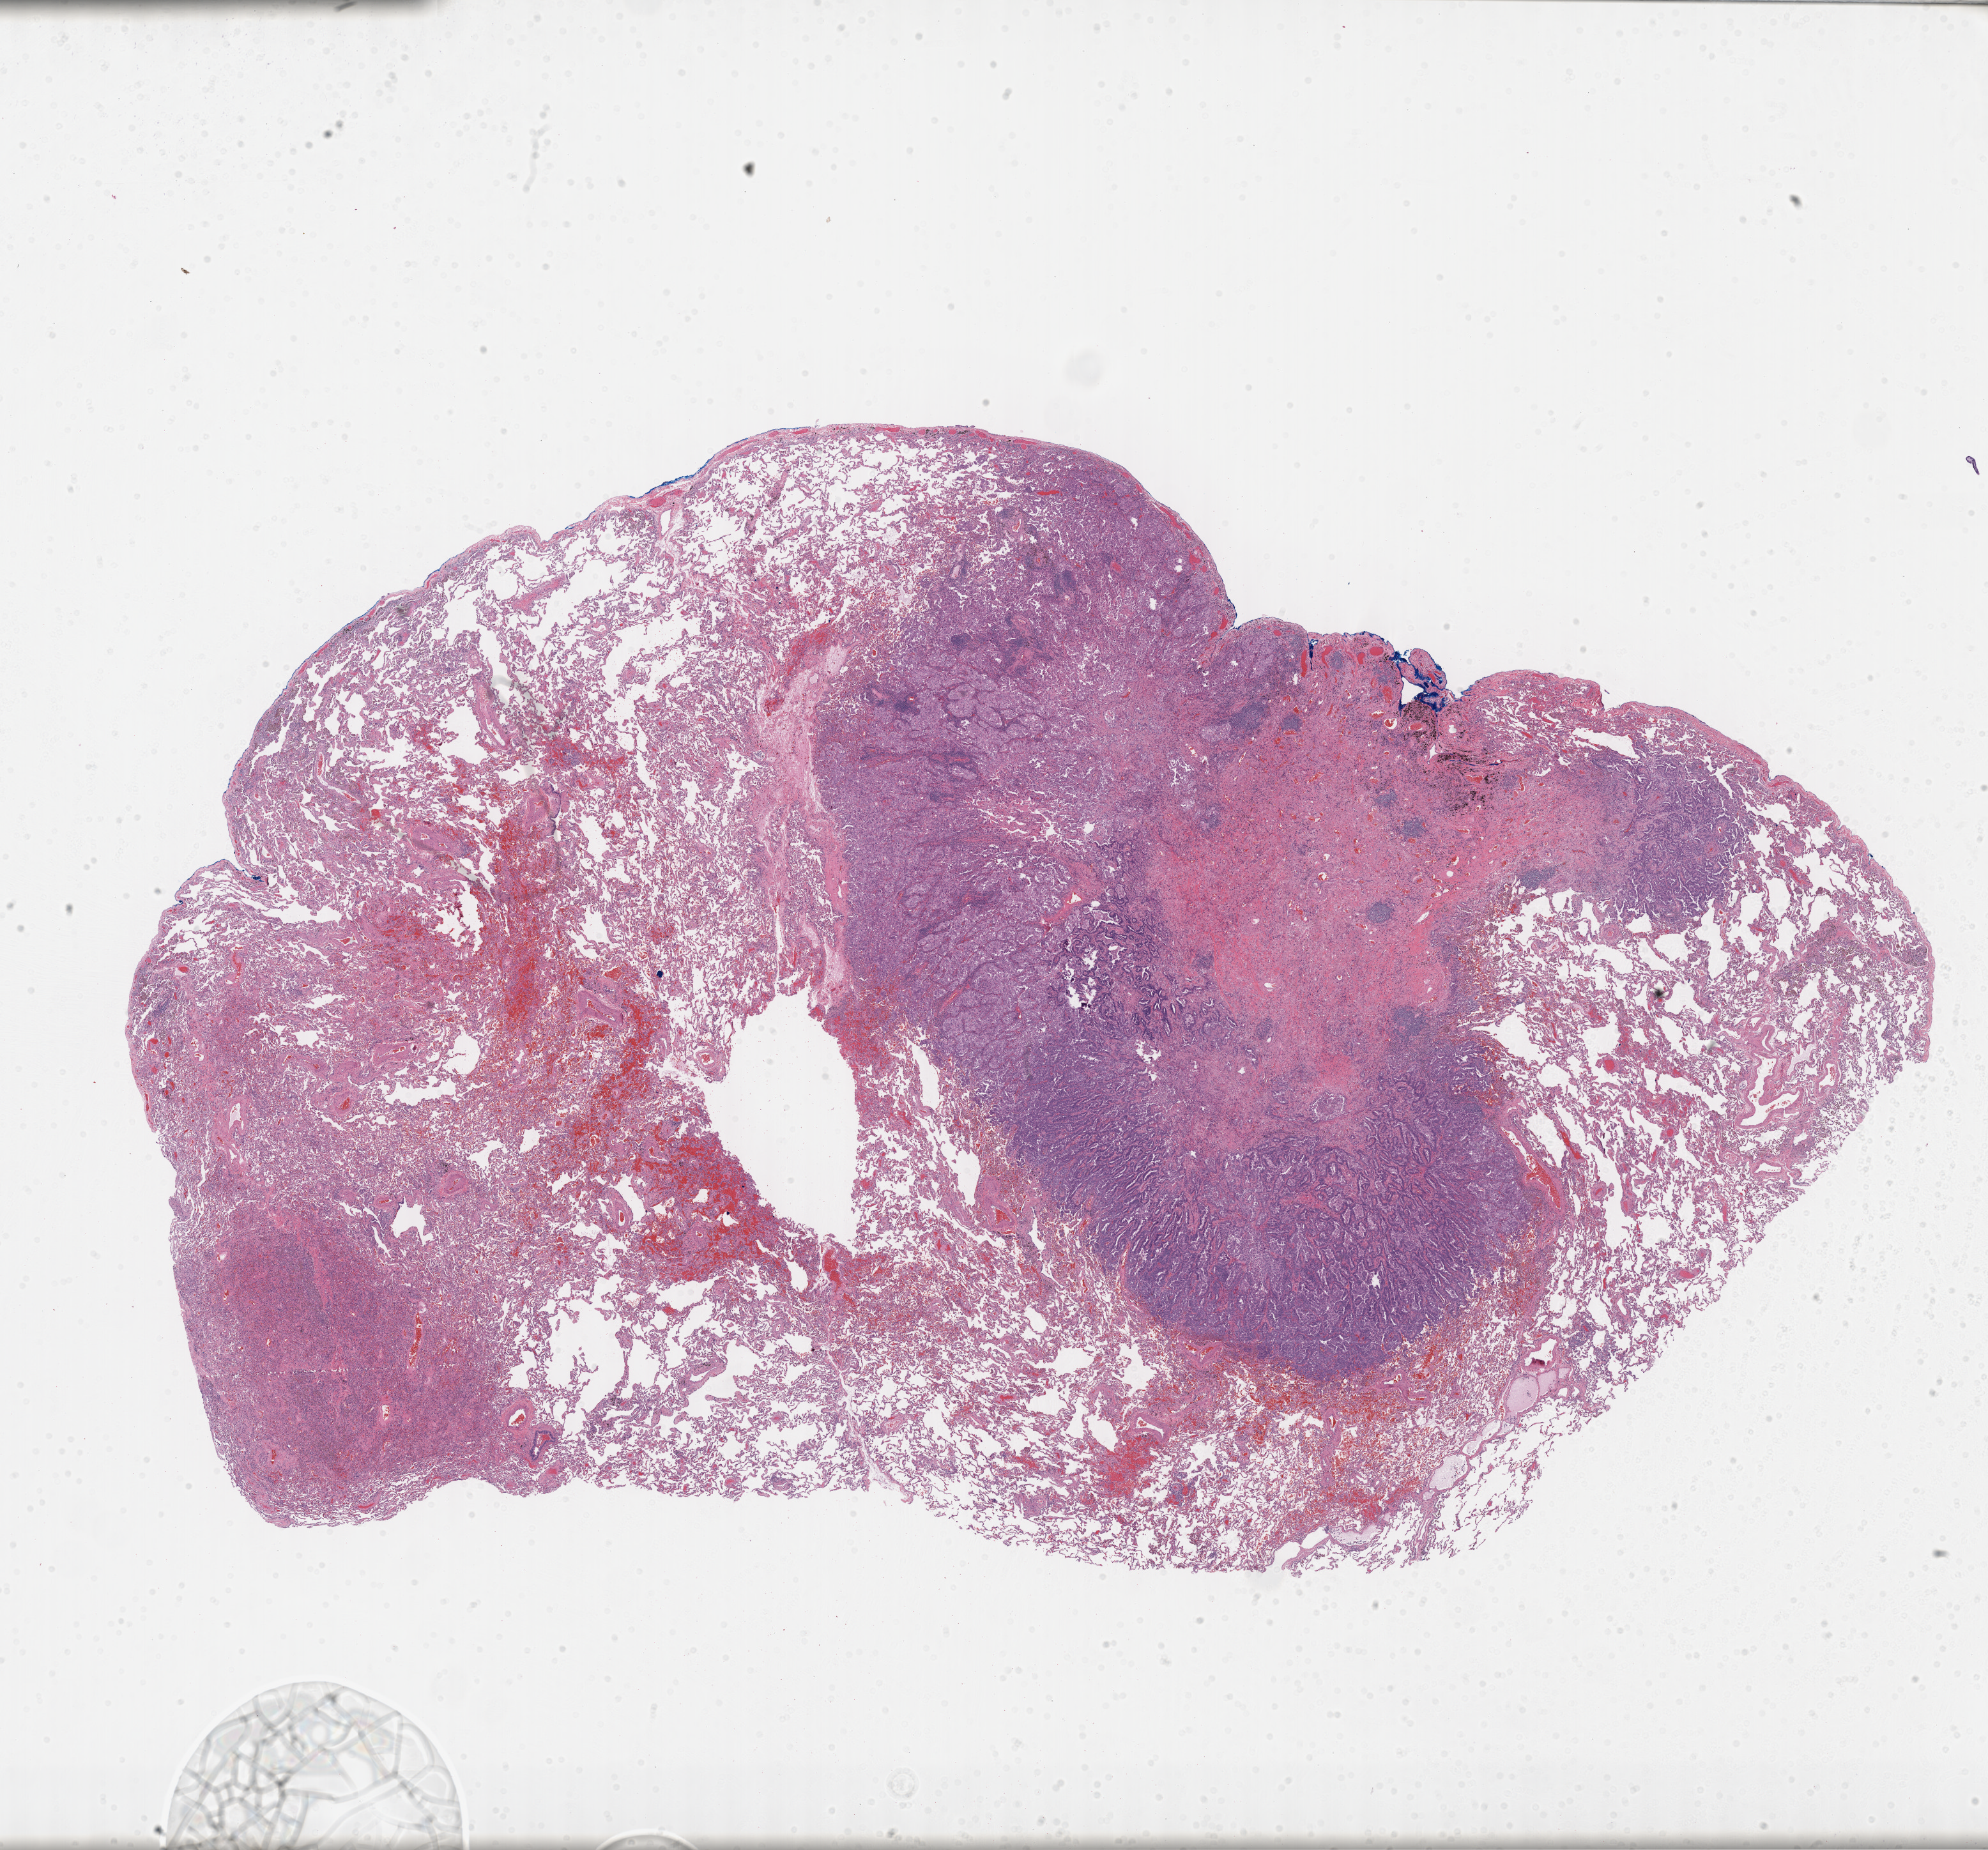
Whole-slide histology image, Hematoxylin and eosin (H&E) stained, whole scanned area (about 25.2 x 23.4 mm, acquisition: 40x scan) shown as a low-resolution overview; formalin-fixed paraffin-embedded (FFPE) diagnostic section; primary tumour sample from the lung. Patient: male, age at initial diagnosis 63 years.
* diagnosis: Adenocarcinoma, NOS (upper lobe, lung)
* laterality: left
* AJCC pathologic stage: IA (7th edition)